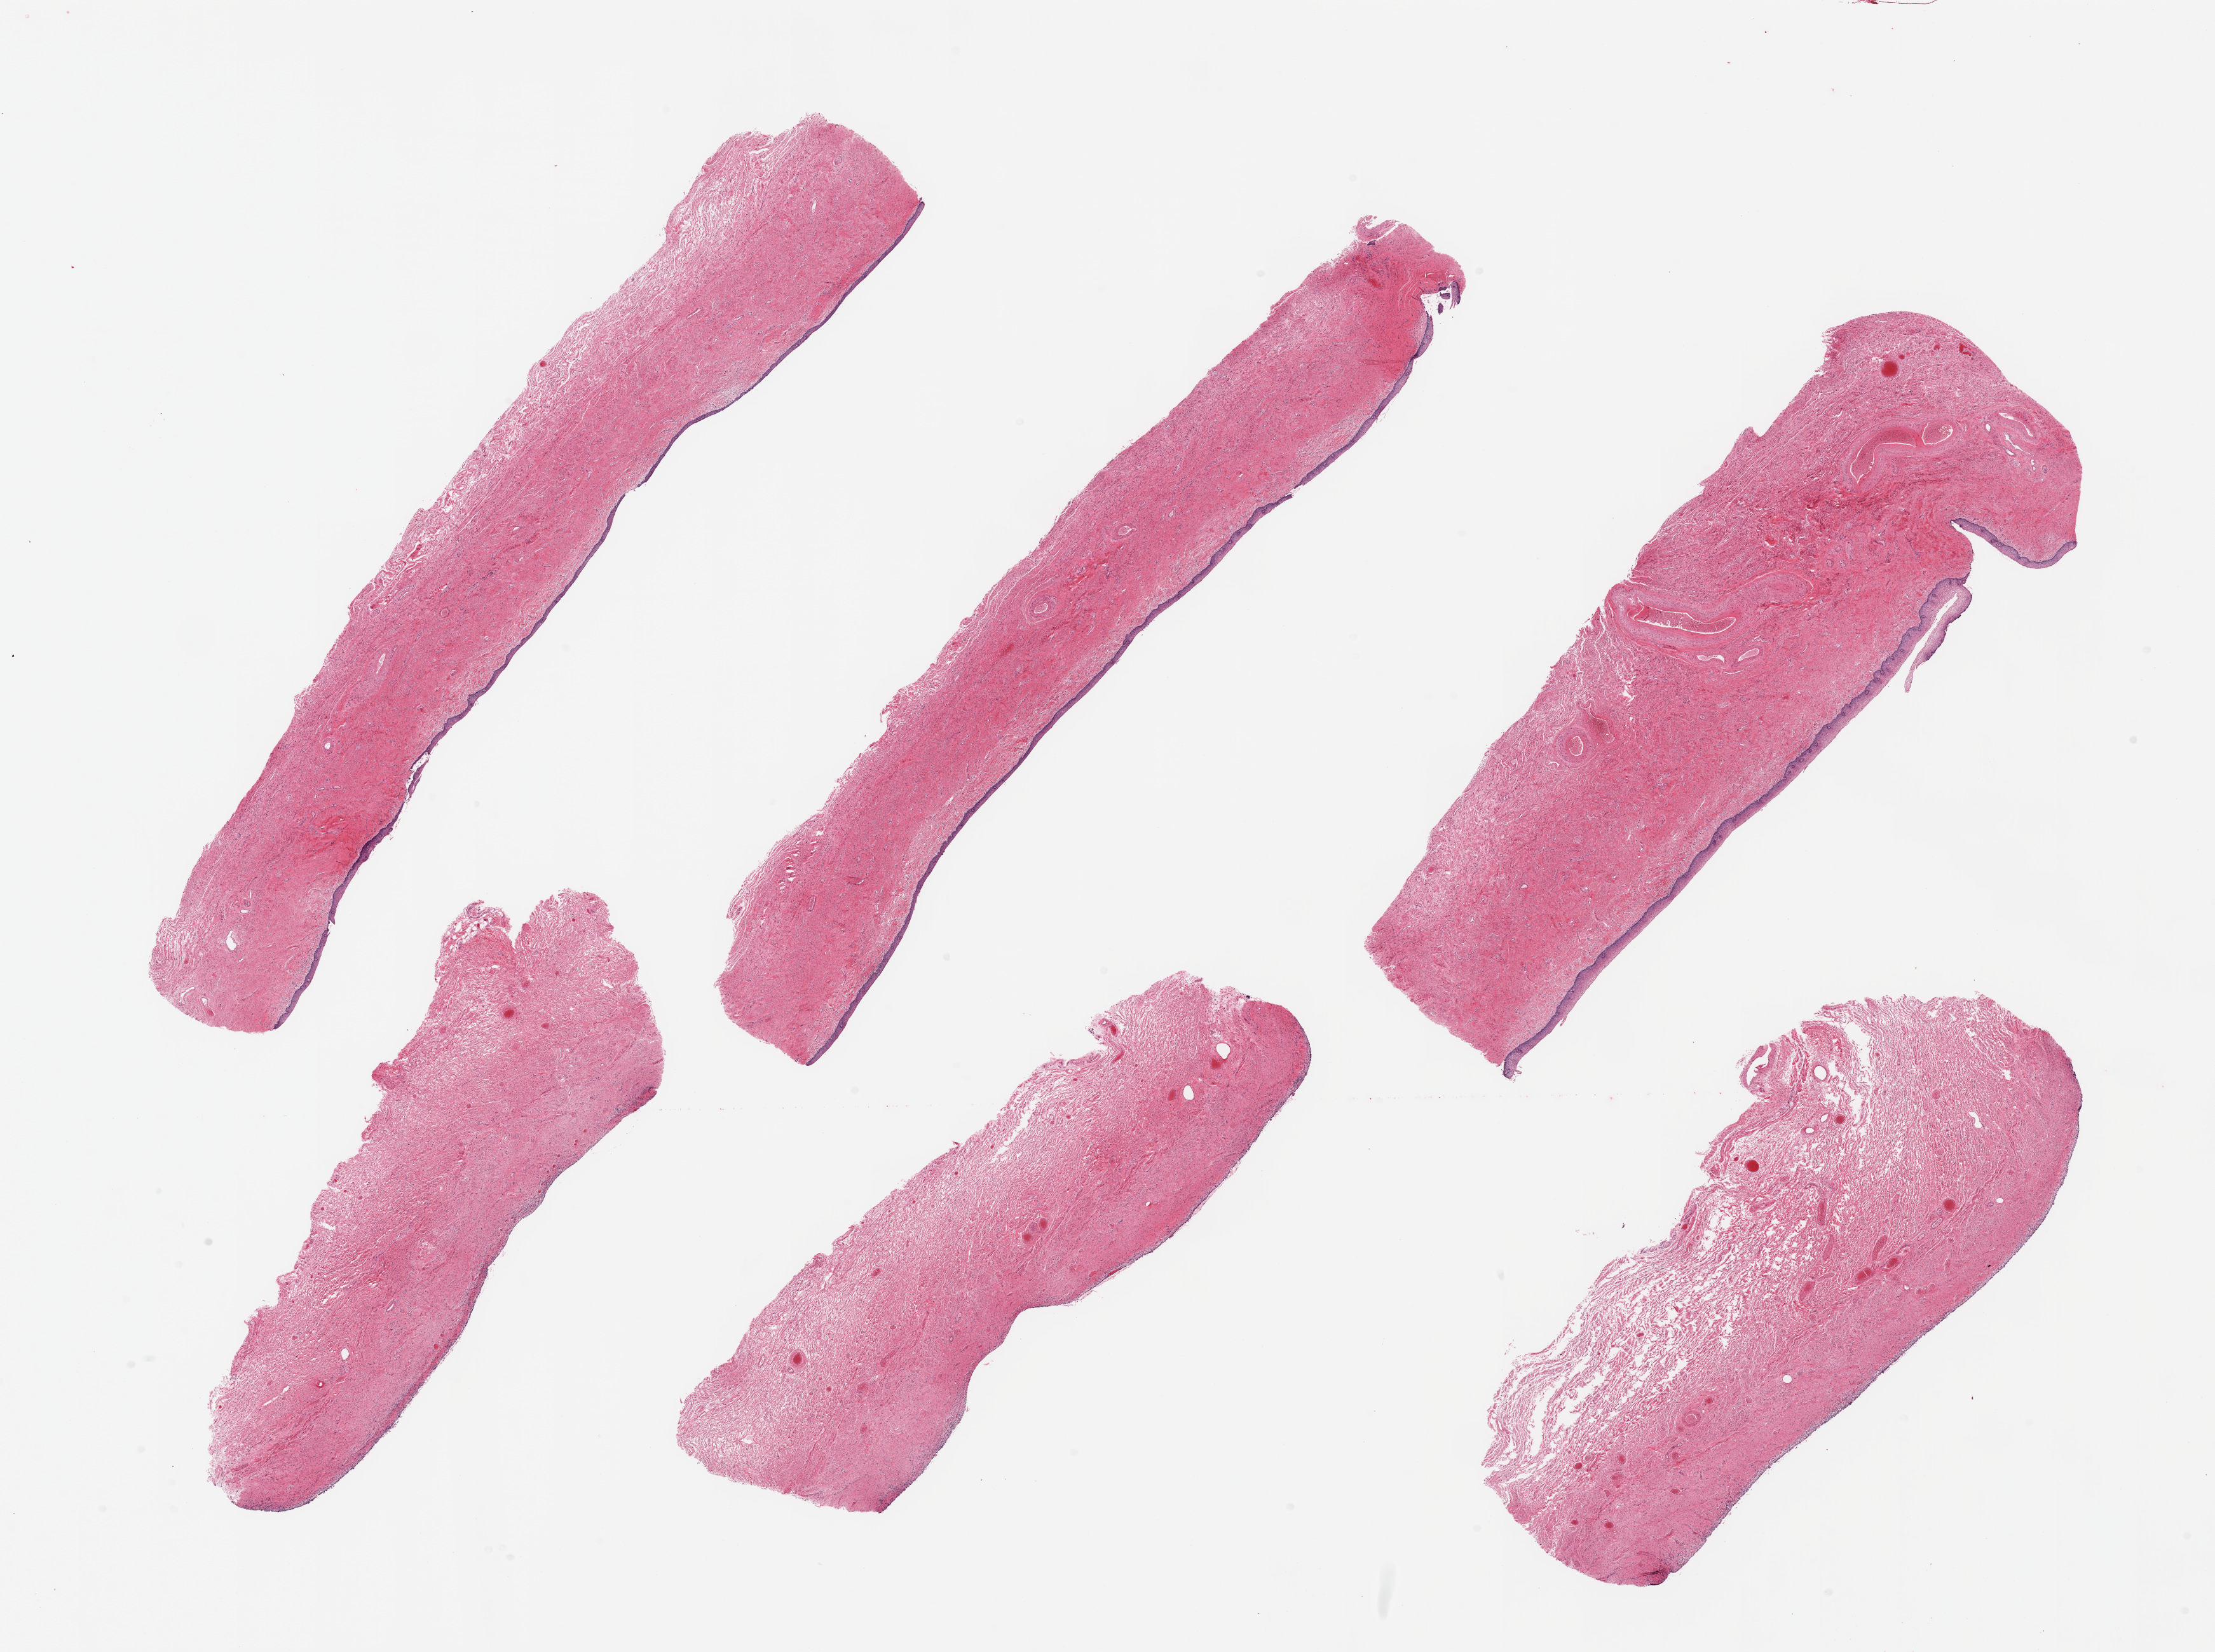
Whole-slide image, haematoxylin and eosin stain — a low-resolution overview of the entire scanned area, about 27.6 x 20.6 mm; PAXgene-fixed, paraffin-embedded tissue; target tissue: vagina; tissue donor sample.
Reviewer comment on this tissue sample: 6 pieces; atrophic surface epithelium on all with almost complete sloughing on 3.